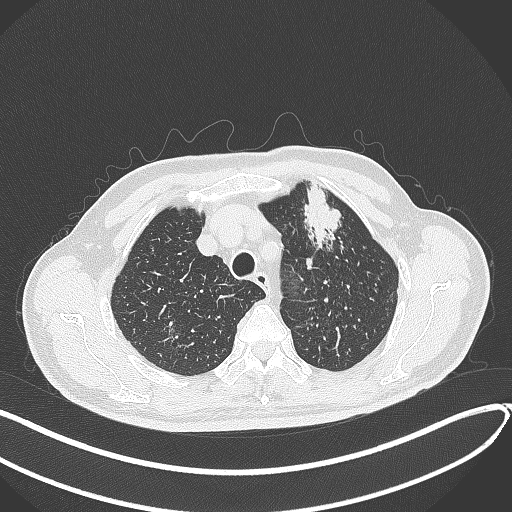
Chest CT, one axial slice. Position 343 of 459 along the scan axis. Reconstruction kernel B70f. 120 kVp. Lung window (W 1500 / L -600 HU). 512 × 512 image matrix. Patient: male, 74 years. Case-level facts recorded for this patient, not image findings: clinical TNM (as recorded): T2b N0 M1c.
Structures marked on this image (bounding box drawn by a radiologist):
- lung tumour (recorded histology: adenocarcinoma): bounding box <298,180,346,253> (left, top, right, bottom; pixels)